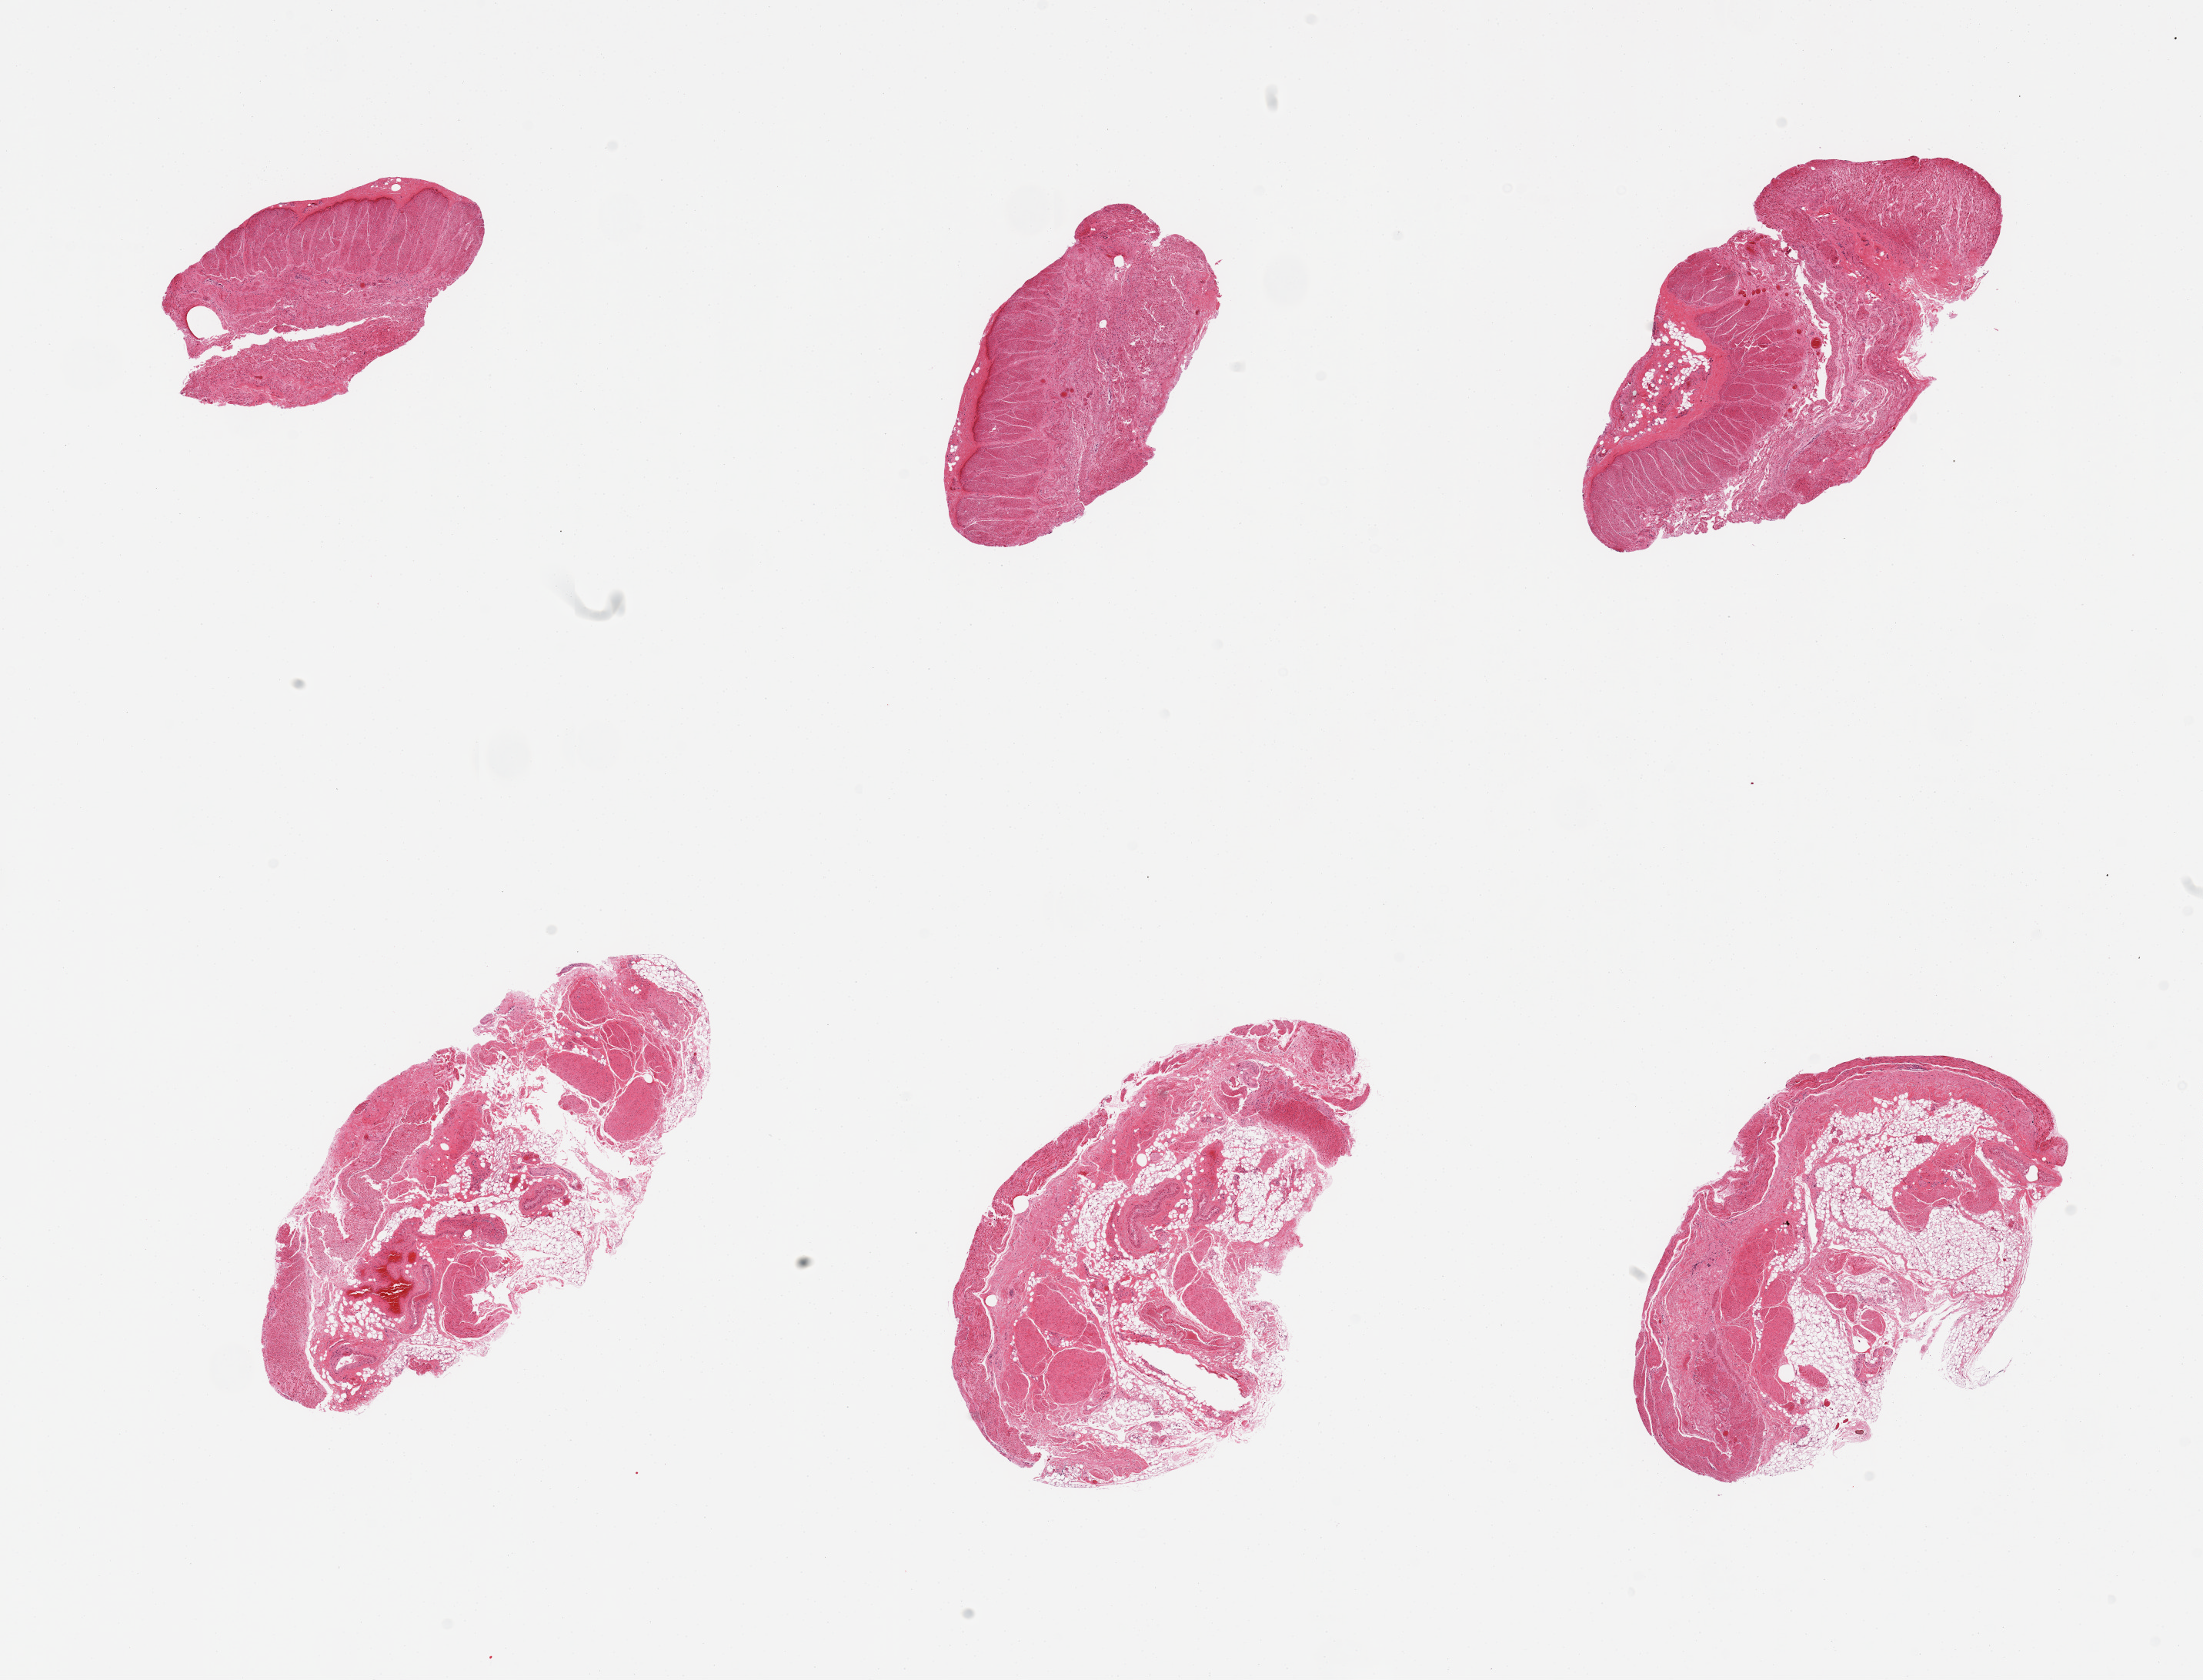
Digitized hematoxylin and eosin (H&E)-stained section, brightfield, a low-resolution overview of the entire scanned area, about 22.6 x 17.3 mm; PAXgene-fixed paraffin-embedded (PFPE) section; section of ileum (target tissue); donor tissue sample. Donor sex: male.
Pathologist's review note for this sample: 6 pieces, muscularis/adipose tissue, no mucosa/lymphoid tissue.